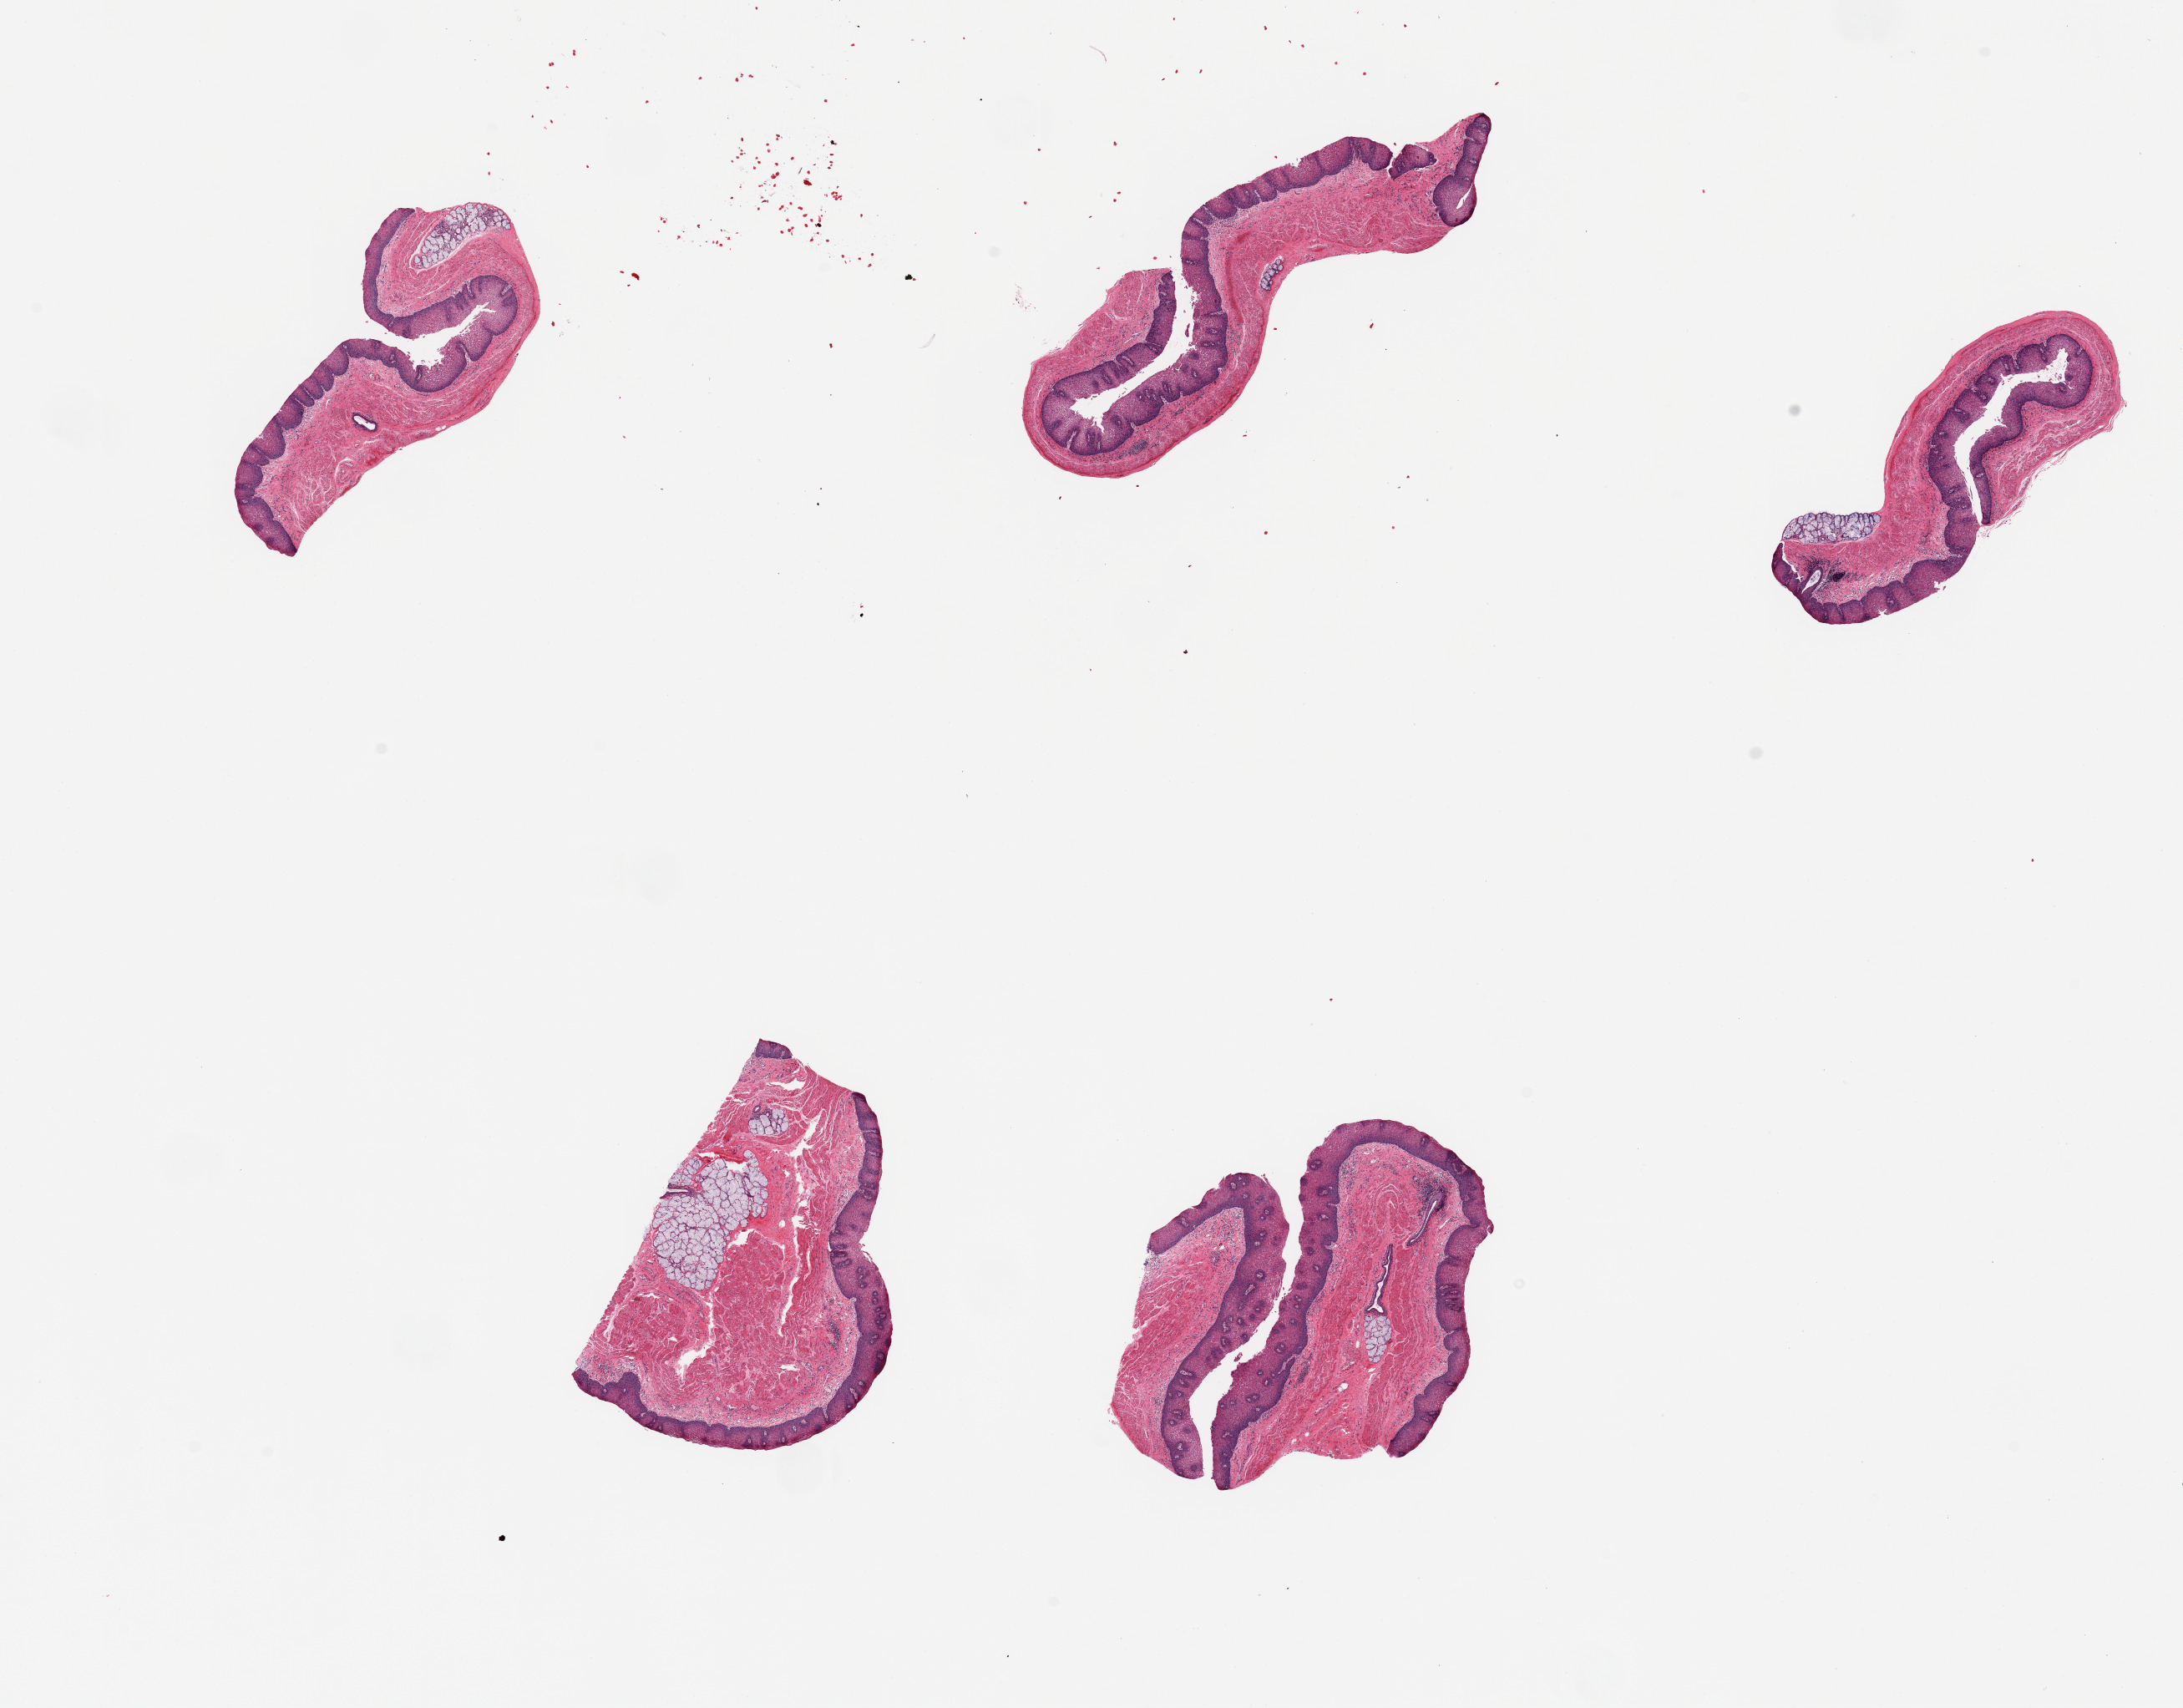
Whole-slide image, haematoxylin and eosin stain — whole scanned area (about 20.7 x 16.2 mm, from a 20x scan) shown as a low-resolution overview, PAXgene-fixed paraffin-embedded (PFPE) section, section of esophageal mucous membrane (target tissue), tissue donor sample. Male donor.
* pathologist's review note for this sample: 5 pieces; several clusters of submucosal glands present, patchy mild chronic inflammation and eosinophilic squamous surface